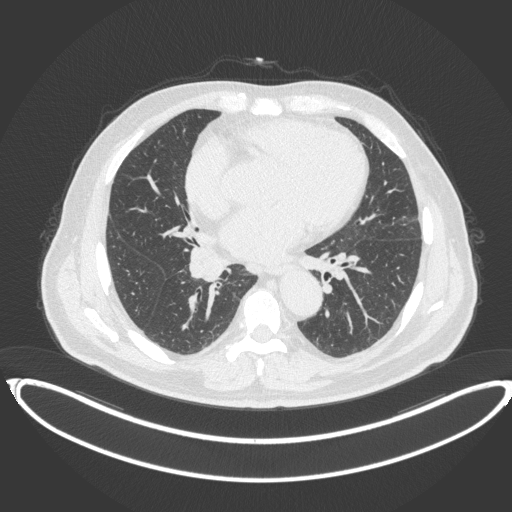
Chest CT, one axial slice. Position 191 of 383 along the scan axis. Reconstruction kernel B31f. Lung window (W 1500 / L -600 HU). 1 mm slice thickness. 512 × 512 image matrix. Patient: male, 61 years. Case-level facts recorded for this patient, not image findings: clinical TNM (as recorded): T1b N1 M0.
Annotated regions visible in this slice (rectangle marked by the reading radiologist):
- lung tumour (recorded histology: squamous cell carcinoma): bounding box (x1, y1, x2, y2) in pixels: (188, 245, 226, 283)